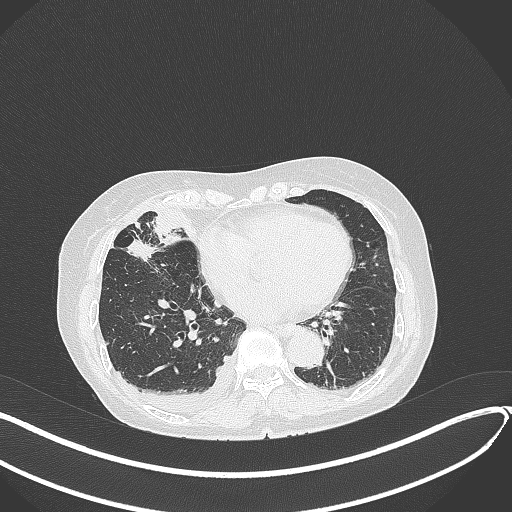
Chest CT, one axial slice; slice 146 of 418 in the series (ordered by position); reconstruction kernel B70f; lung window (W 1500 / L -600 HU); 1 mm slice thickness; 512 × 512 image matrix, field of view 400 × 400 mm. Female patient, age 75 years. From the clinical record (not read from this slice): clinical TNM (as recorded): T2a N3 M0.
Structures marked on this image (bounding box drawn by a radiologist):
- lung tumour (recorded histology: adenocarcinoma): bounding box [x1, y1, x2, y2] px = [125, 236, 159, 264]